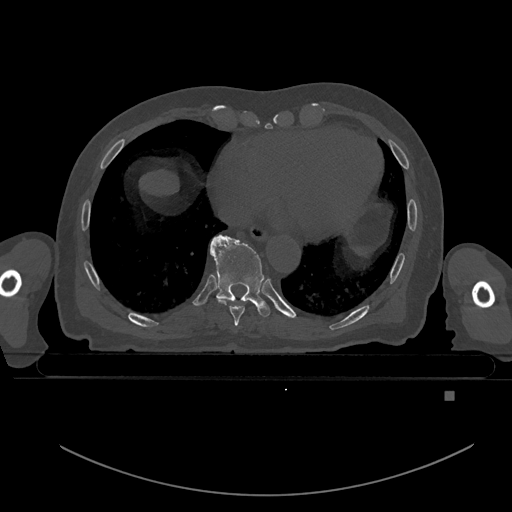
CT including the spine, one axial slice; slice 168 of 969 in the series (ordered by position); bone window (W 1800 / L 400 HU); 0.5 mm slice thickness; 512 × 512 image matrix. Male patient, age 82 years. Case-level facts recorded for this patient, not image findings: primary cancer: prostate; vertebrae with lytic lesions (as recorded): T11, T9, T8, T2.
Outlined on this slice (semi-automatic segmentation, software-assisted and operator-edited):
- T8 vertebra: box from (x=215, y=297) to (x=251, y=326) px
- T9 vertebra: (x=210, y=235)–(x=271, y=317)